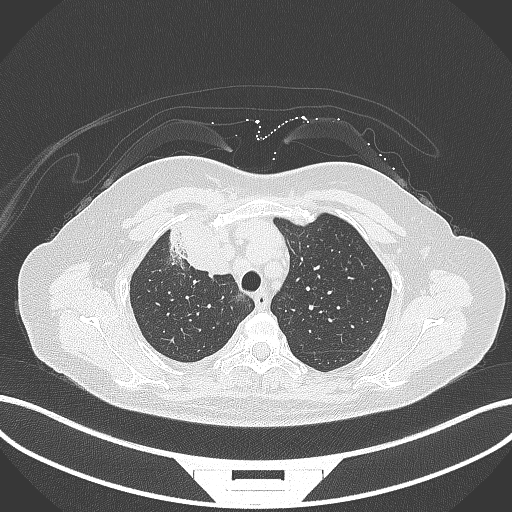
Chest CT, one axial slice. Slice 237 of 305 in the series (ordered by position). Lung window (W 1500 / L -600 HU). 1 mm slice thickness. 512 × 512 image matrix. Female patient, age 52 years. Case-level facts recorded for this patient, not image findings: clinical TNM (as recorded): T3 N1 M1.
Outlined on this slice (bounding box drawn by a radiologist):
- lung tumour (recorded histology: adenocarcinoma): bounding box <162,218,232,277> (left, top, right, bottom; pixels)